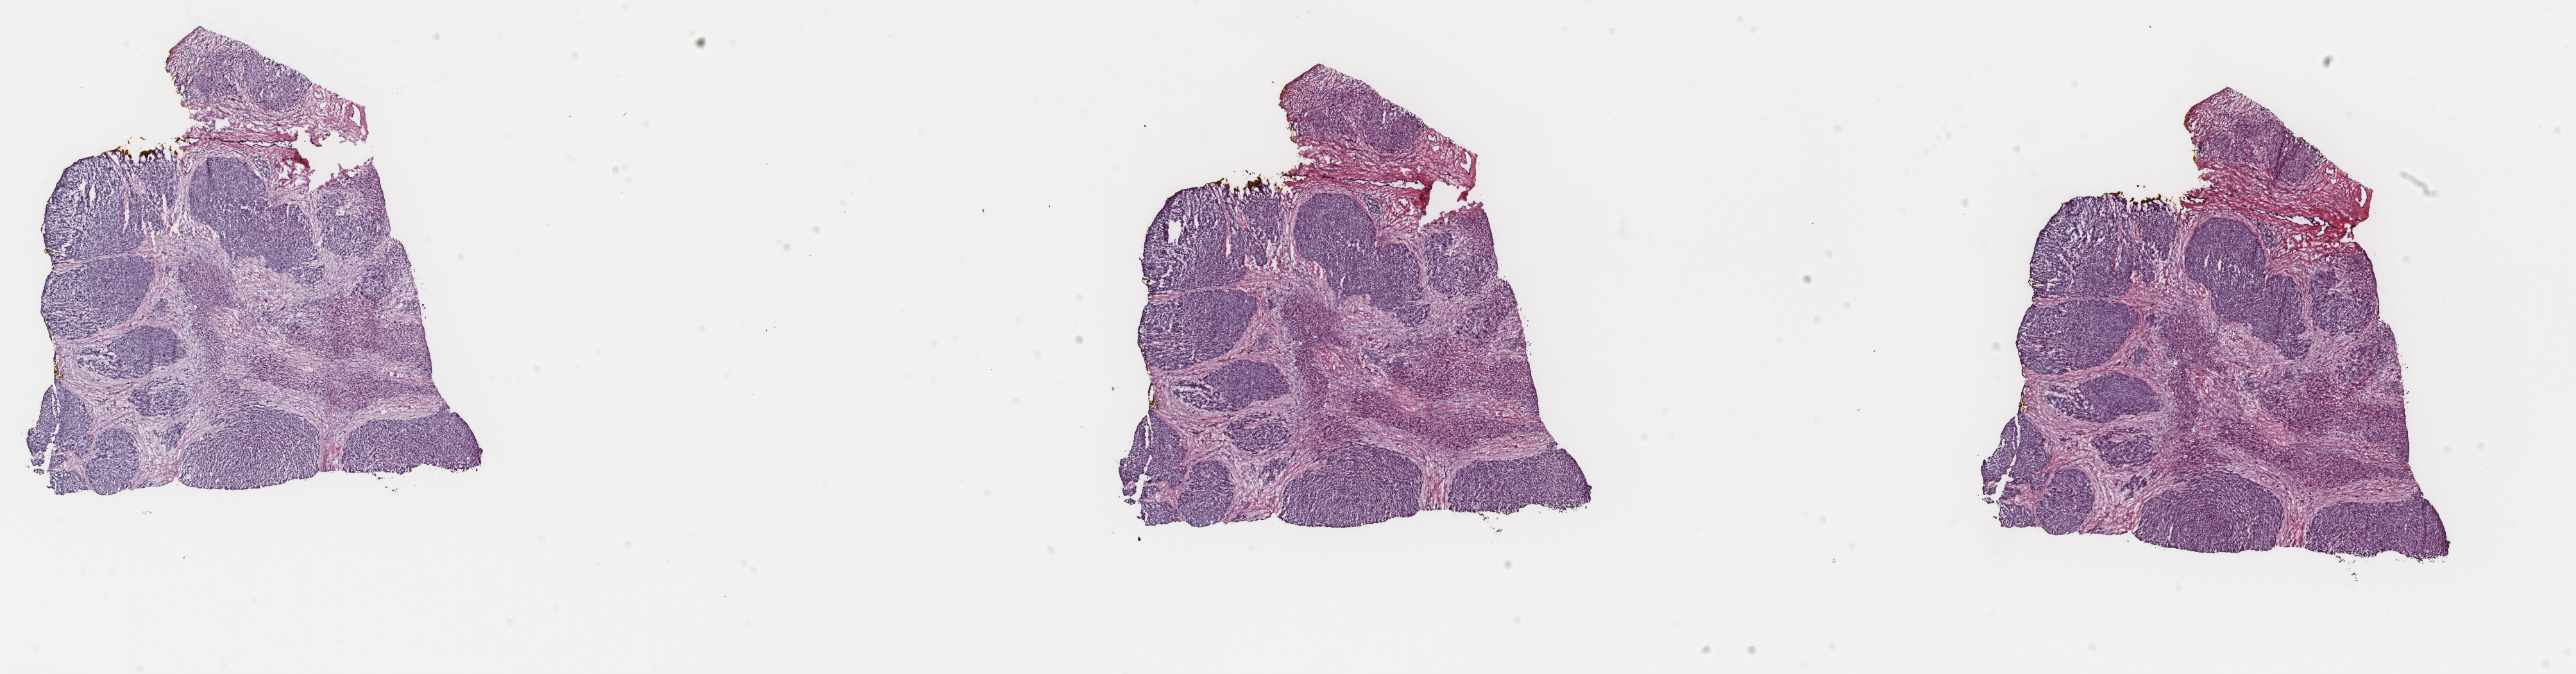
Digitized H&E-stained tissue section (whole slide), a low-resolution overview of the entire scanned area, about 31.9 x 8.3 mm (slide scanned at 40x), frozen section from the top of the tissue portion, sample: primary tumour, liver. Female patient; age at initial diagnosis 51 years. Histologic grade: G2 (moderately differentiated). Slide review estimates, as recorded: tumour cells 70%, tumour nuclei 70%, normal cells 0%, stromal cells 30%, necrosis 0%. Infiltration values recorded for this section: lymphocyte infiltration 5%, monocyte infiltration 0%, neutrophil infiltration 0%.
* diagnosis: Hepatocellular carcinoma, NOS
* AJCC pathologic stage: II